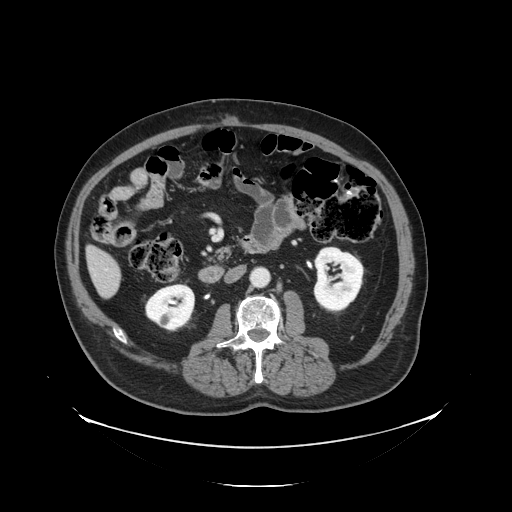
Contrast-enhanced abdominal CT, one axial slice. Slice 39 of 138 in the series (ordered by position). Reconstruction kernel STANDARD. 120 kVp. Soft-tissue window (W 400 / L 40 HU). 2.5 mm slice thickness. 512 × 512 image matrix, field of view 497 × 497 mm. Male patient, age 77 years. From the clinical record (not read from this slice): diagnosis: colorectal cancer liver metastases, imaged before liver resection; multiple liver metastases: no; largest metastasis: 1.5 cm; disease in both lobes: no.
Outlined on this slice (expert manual segmentation):
- liver: bounding box [x1, y1, x2, y2] px = [89, 249, 121, 297]
- planned liver remnant (the part of the liver to remain after resection): [89, 249, 118, 276]